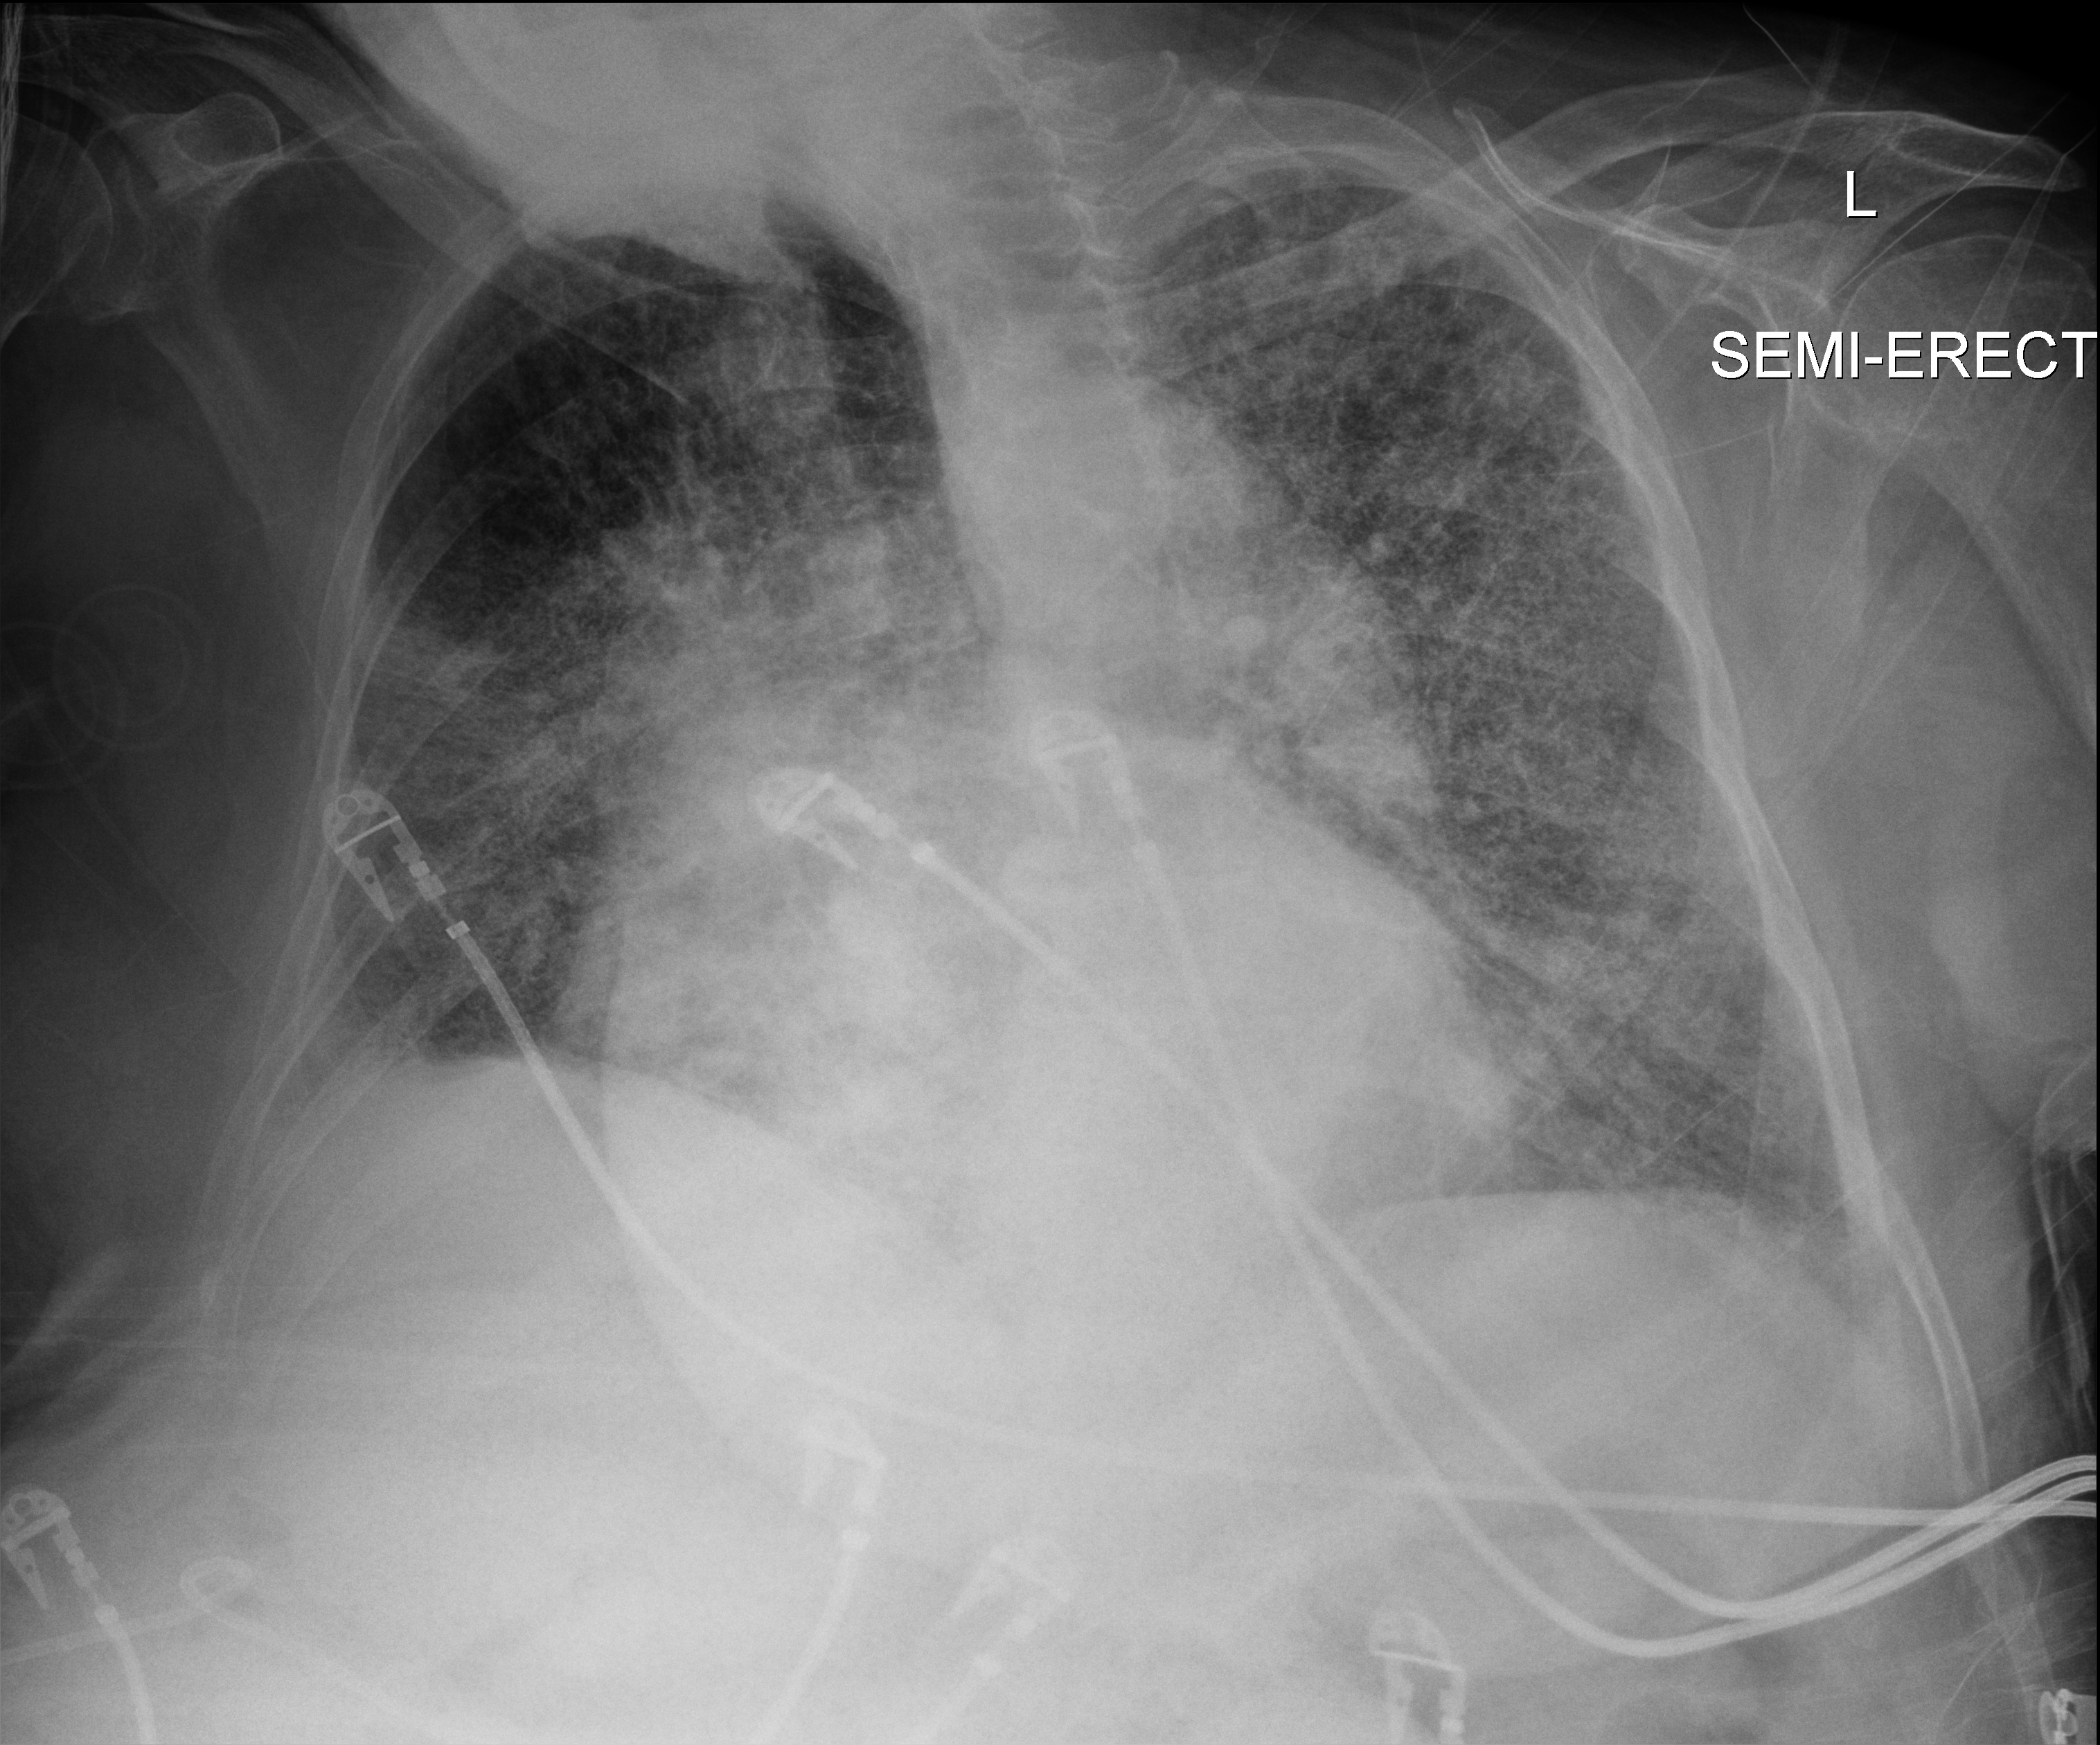
Portable chest radiograph, anteroposterior (AP) projection. Female patient hospitalised with COVID-19, age 75–90 years.
Admission-level facts for this patient (not findings on this image; timing relative to this image not recorded): mechanically ventilated during this hospital stay: no; diabetes (admission record): yes; admitted to intensive care during this hospital stay: no.